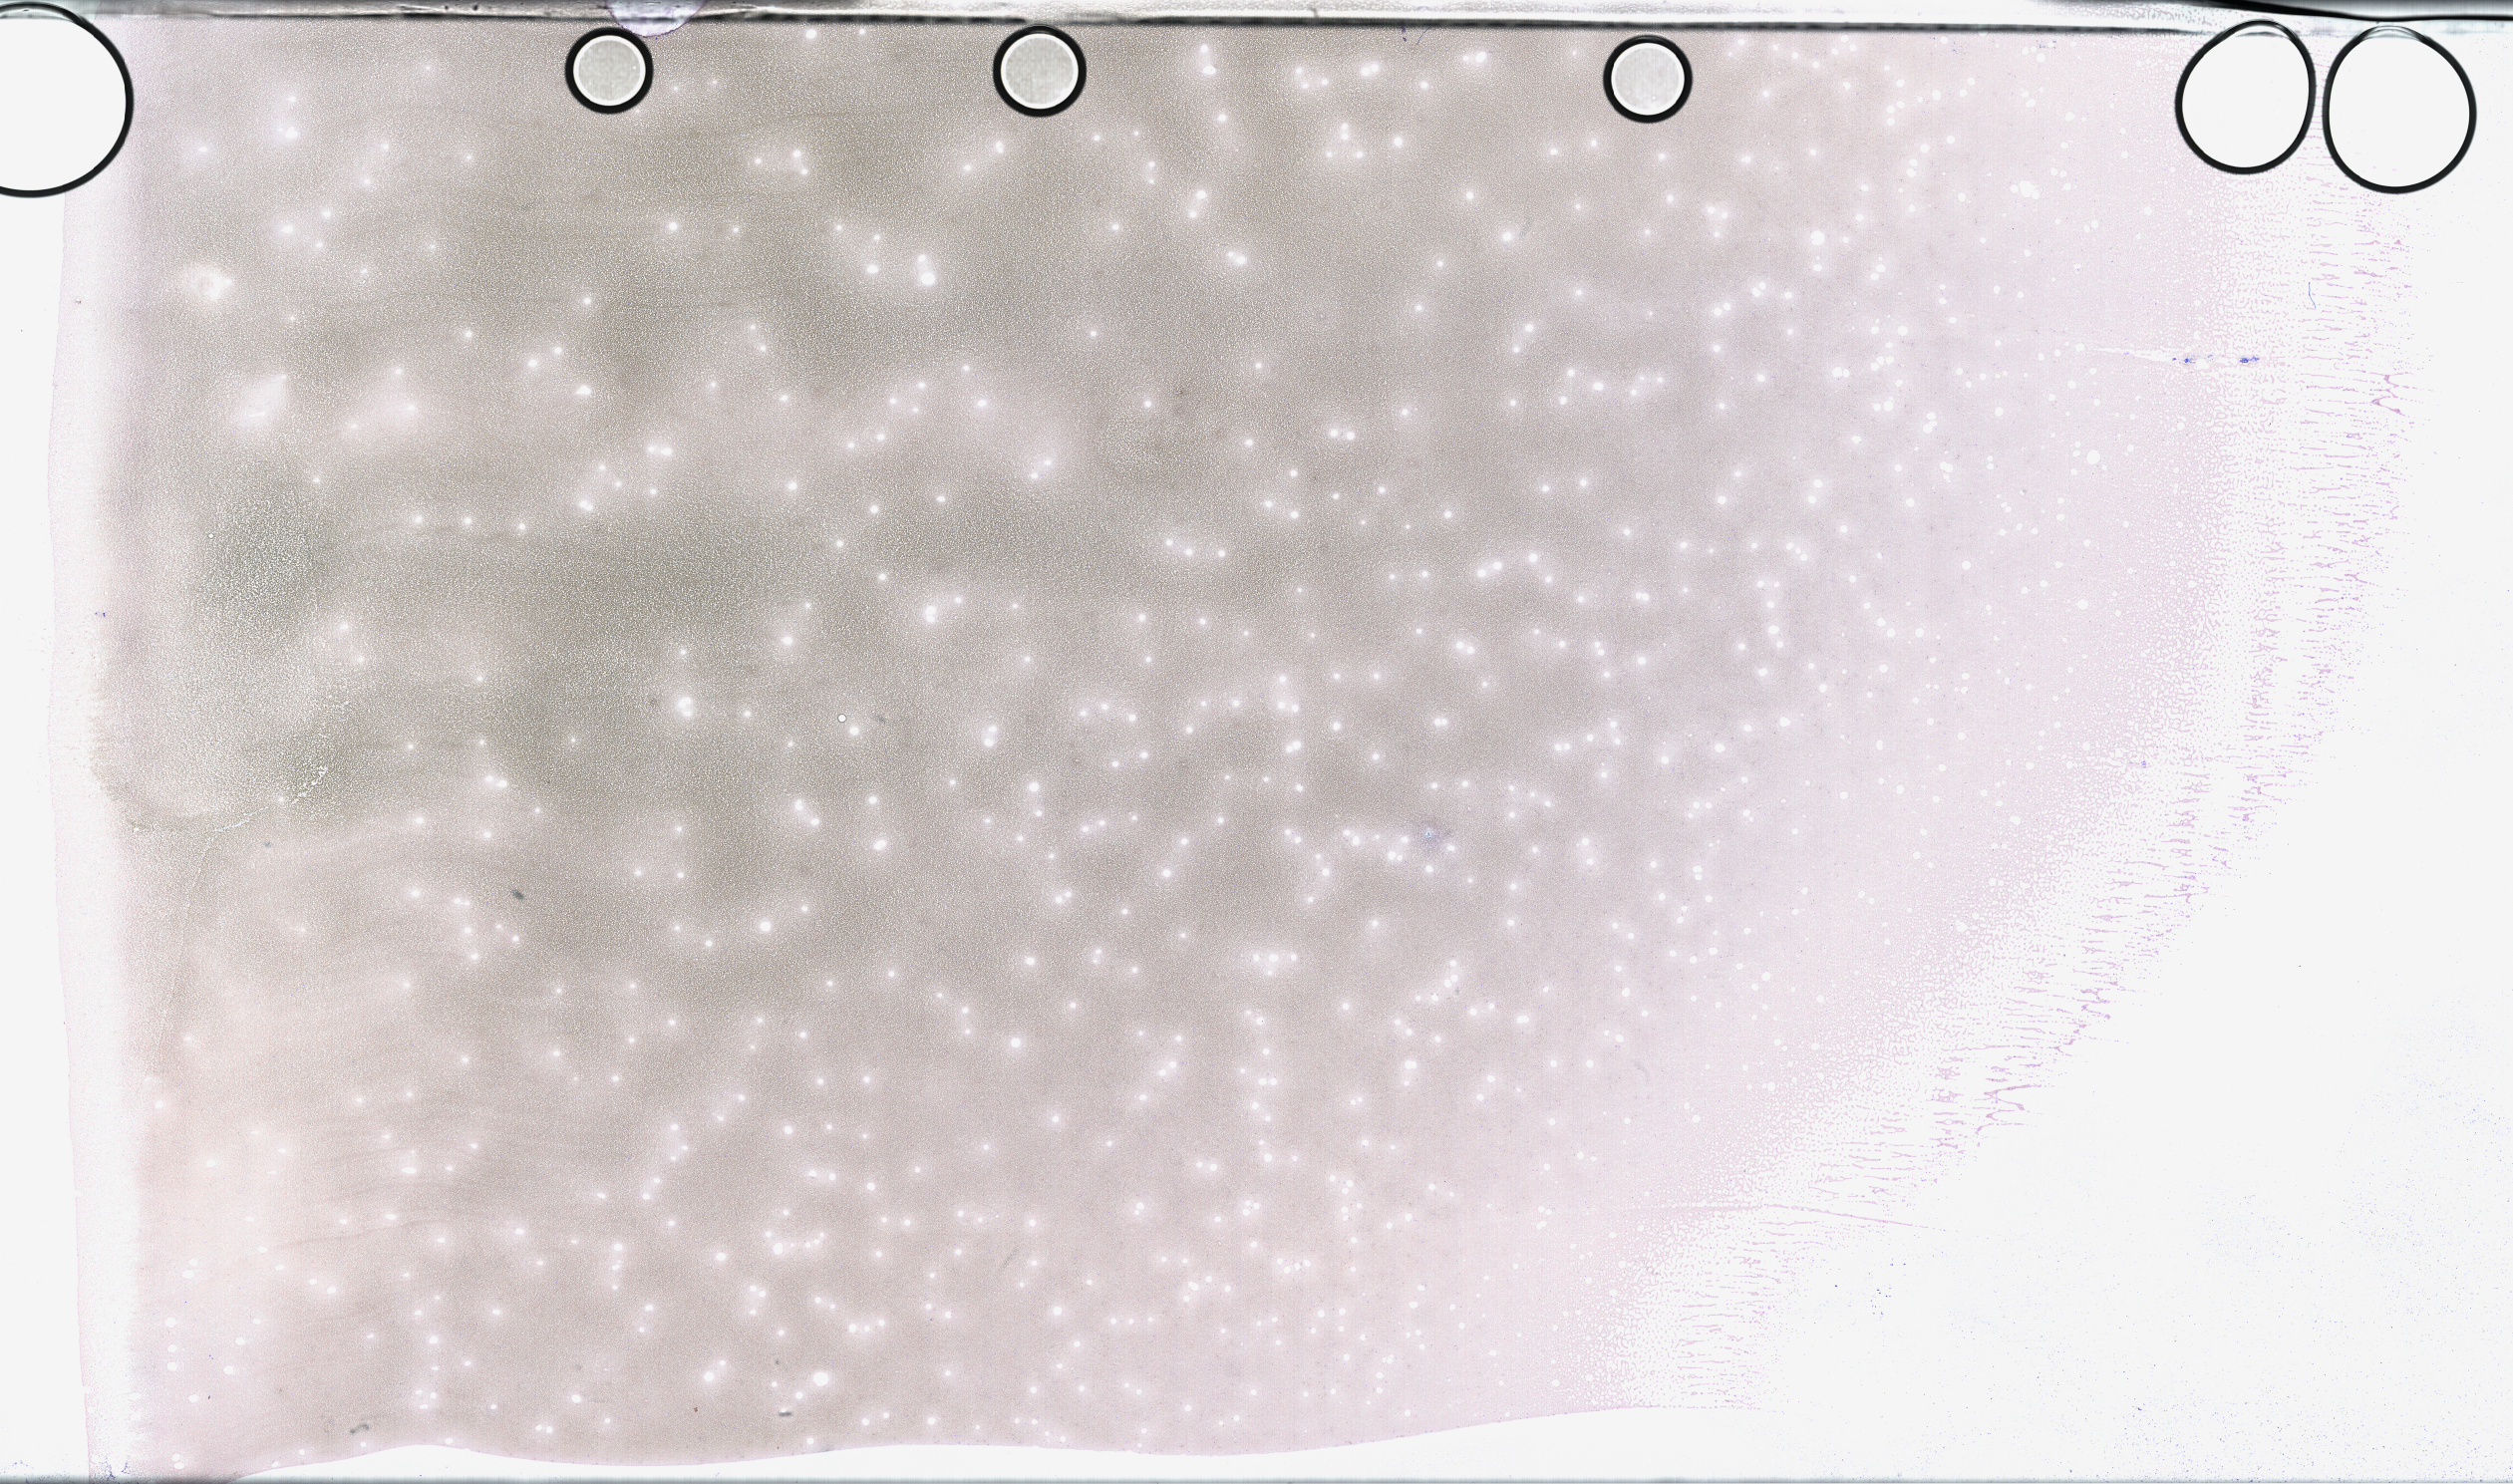
Whole-slide image of a whole blood smear, Wright–Giemsa stain, a low-resolution overview of the entire scanned area, about 40.7 x 24.0 mm. Smear from an EDTA sample. Patient sex: female.
From a patient with: Plasma Cell Myeloma.